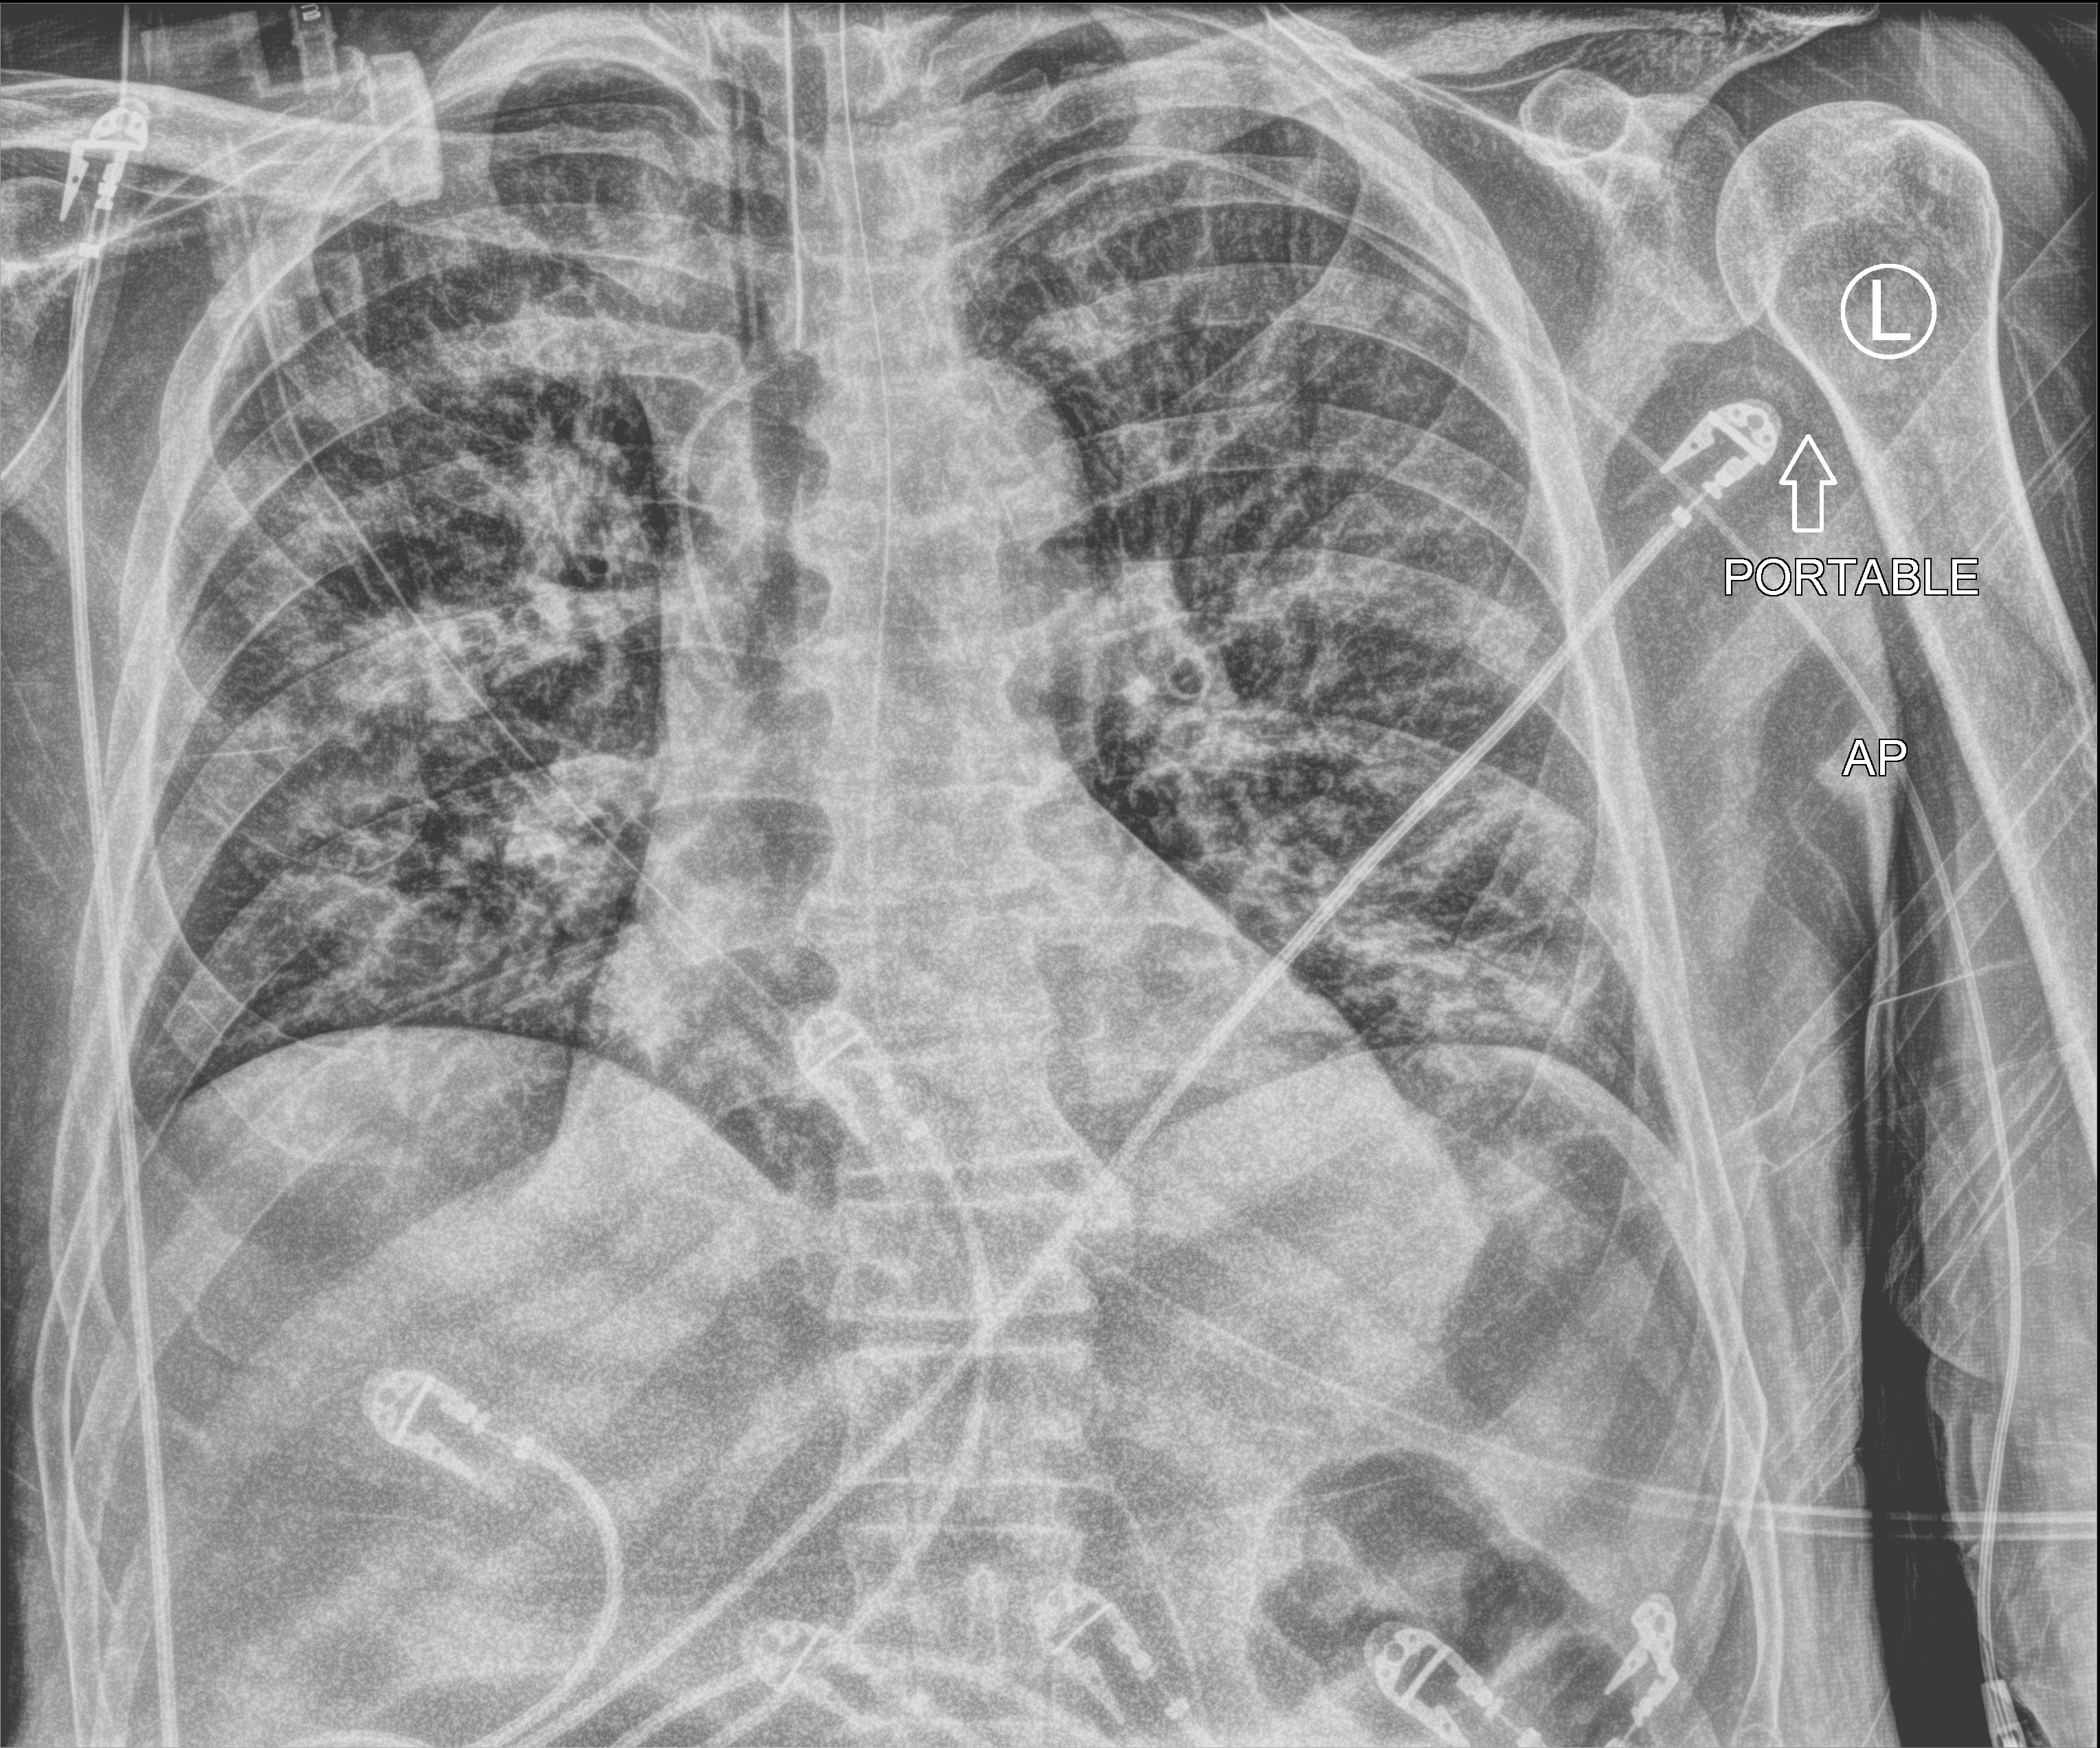
Portable chest radiograph, anteroposterior (AP) projection. Patient hospitalised with COVID-19; male, aged 60–74 years.
From the hospital-stay record, not from the radiograph (when in the stay this image was taken is not recorded):
- mechanically ventilated during this hospital stay: yes
- admitted to intensive care during this hospital stay: yes
- length of hospital stay: 35 days